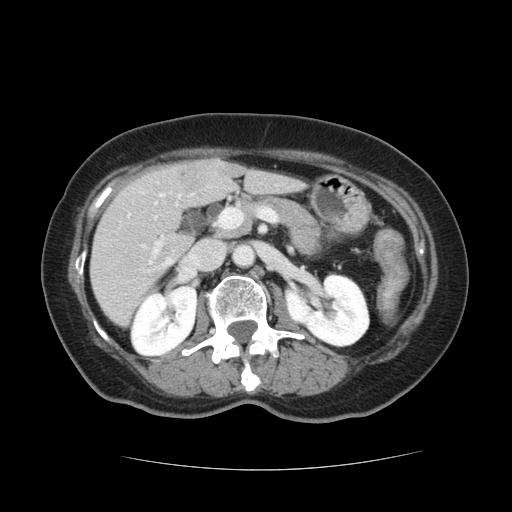
Contrast-enhanced abdominal CT, one axial slice. Position 55 of 128 along the scan axis. 120 kVp. Soft-tissue window (W 400 / L 40 HU). 2.5 mm slice thickness. 512 × 512 image matrix, field of view 366 × 366 mm. Female patient, age 67 years. Case-level facts recorded for this patient, not image findings: diagnosis: colorectal cancer liver metastases, imaged before liver resection; multiple liver metastases: yes; largest metastasis: 3 cm; disease in both lobes: yes.
Outlined on this slice (outlined manually by an expert reader):
- hepatic veins: bounding box <148,257,174,272> (left, top, right, bottom; pixels)
- liver: <92,160,302,326>
- planned liver remnant (the part of the liver to remain after resection): <92,170,301,326>
- portal vein (with intrahepatic branches): <140,211,233,264>